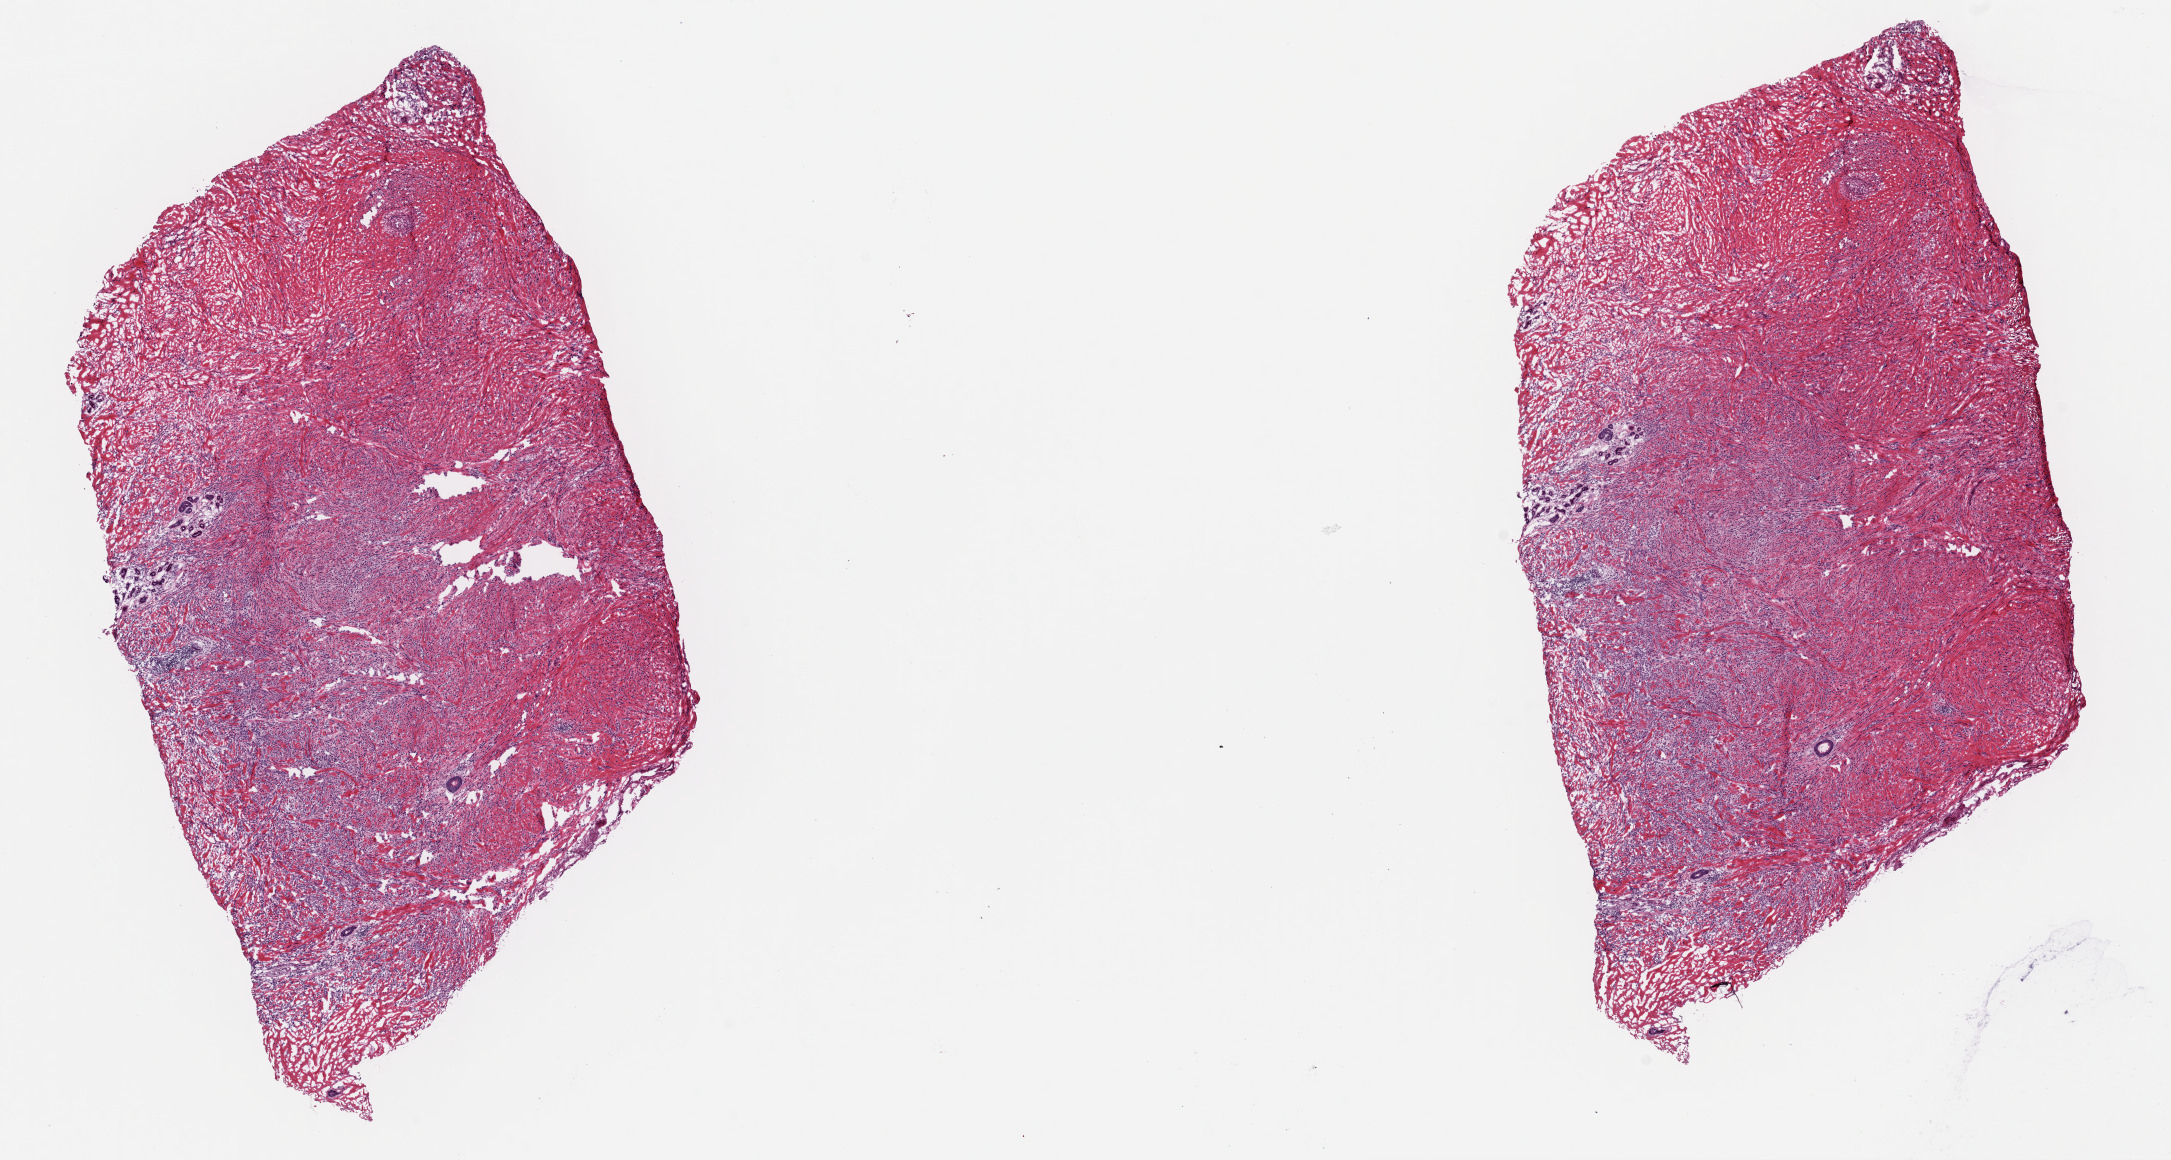
Digitized Hematoxylin and eosin (H&E) stained tissue section (whole slide) — shown as a low-resolution overview of the whole scanned area (about 17.2 x 9.2 mm, acquisition: 40x scan). Frozen section from the top of the tissue portion. Primary tumour sample from the breast. Patient: female, age at initial diagnosis 62 years. Slide review estimates, as recorded: tumour cells 70%, tumour nuclei 70%, normal cells 5%, stromal cells 25%, necrosis 0%. Inflammatory infiltration, as recorded: lymphocyte infiltration 0%, monocyte infiltration 0%, neutrophil infiltration 0%.
Diagnosis: Lobular carcinoma, NOS. Lymph nodes positive (case pathology): 0 of 2 examined. AJCC pathologic stage: IIA. Laterality: right.